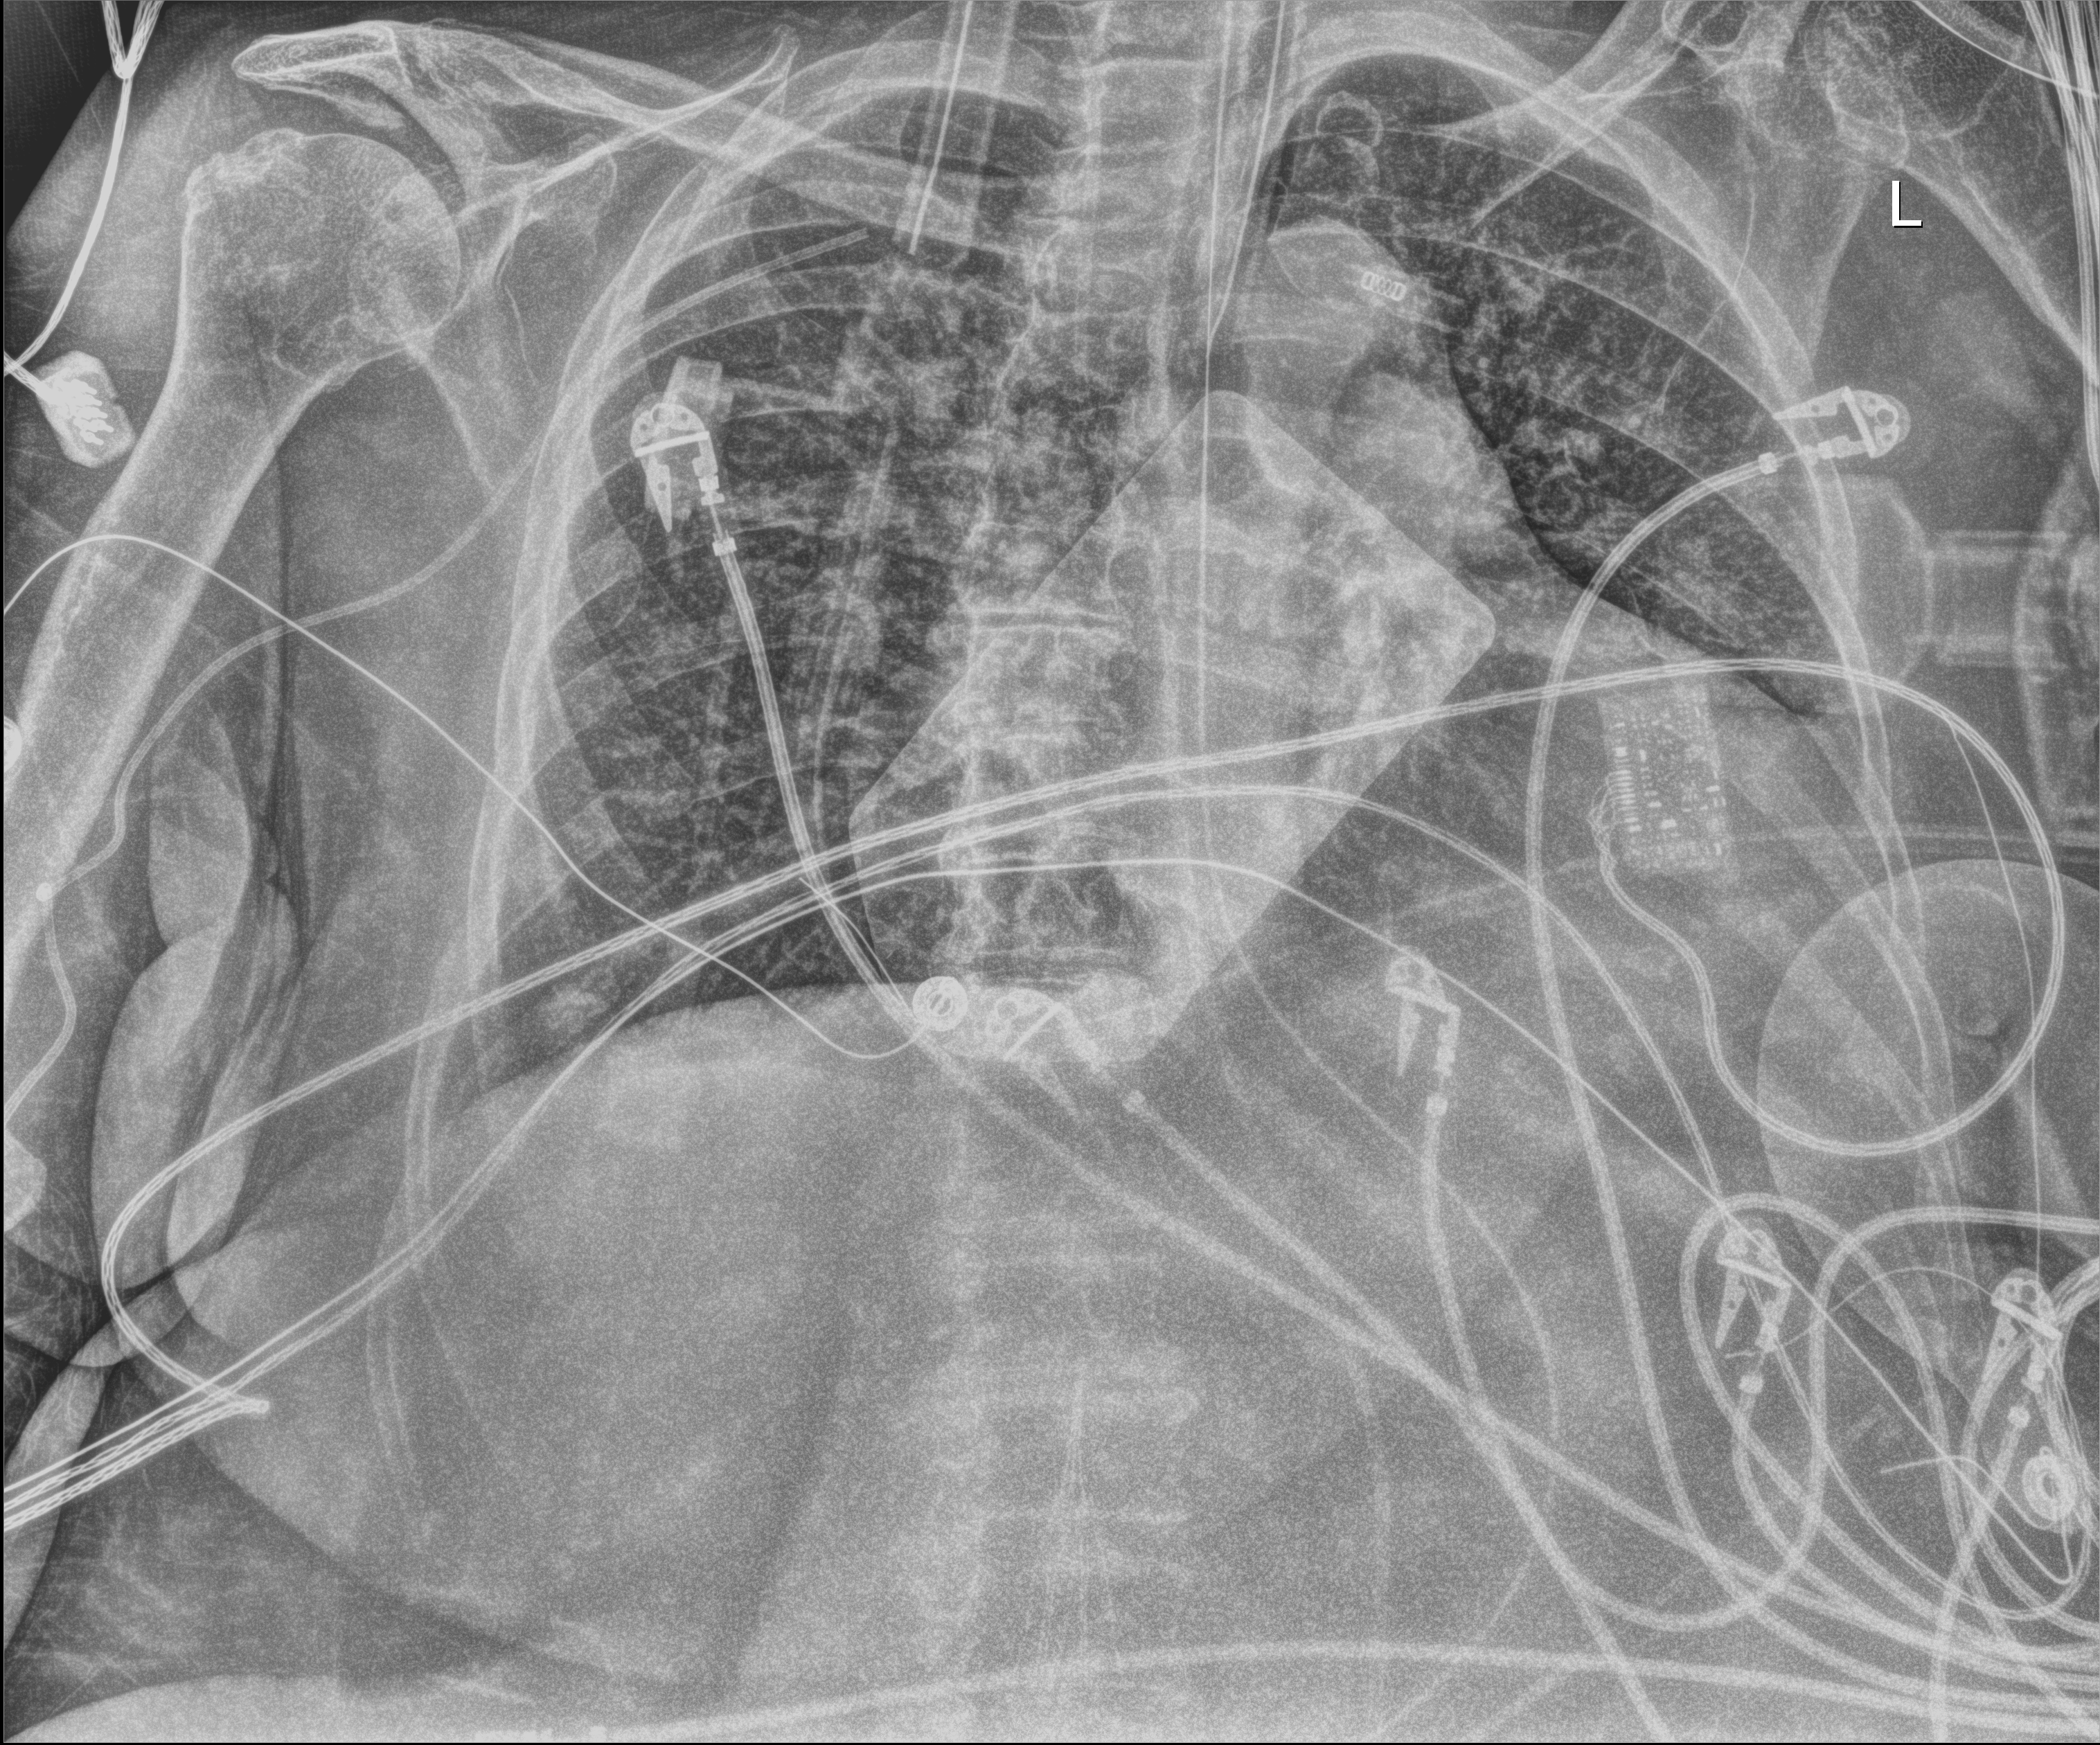
Chest X-ray (portable); anteroposterior (AP) projection. Female patient hospitalised with COVID-19, age 75–90 years.
Admission-level facts for this patient (not findings on this image; timing relative to this image not recorded):
- smoking status (admission record): never